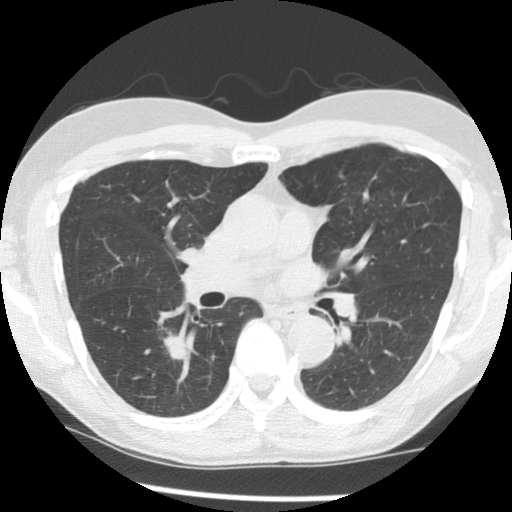
Chest CT (low-dose screening protocol), one axial image; third annual screen; lung window (W 1500 / L -600 HU); standard (soft-tissue) reconstruction kernel (STANDARD); 140 kVp. Male participant, aged 65 years at enrolment. Current smoker at enrolment.
Expert reader's lesion annotation, bounding box [x1, y1, x2, y2] px = [146, 321, 206, 376]. The screening reader recorded 2 non-calcified nodules or masses ≥4 mm on this exam (left lower lobe, right lower lobe); which of them this box marks is not recorded. Later outcome: lung cancer diagnosed 116 days after this screen — adenocarcinoma, NOS, right lower lobe, poorly differentiated (G3), stage IA (AJCC 6th edition), 18 mm at pathology.